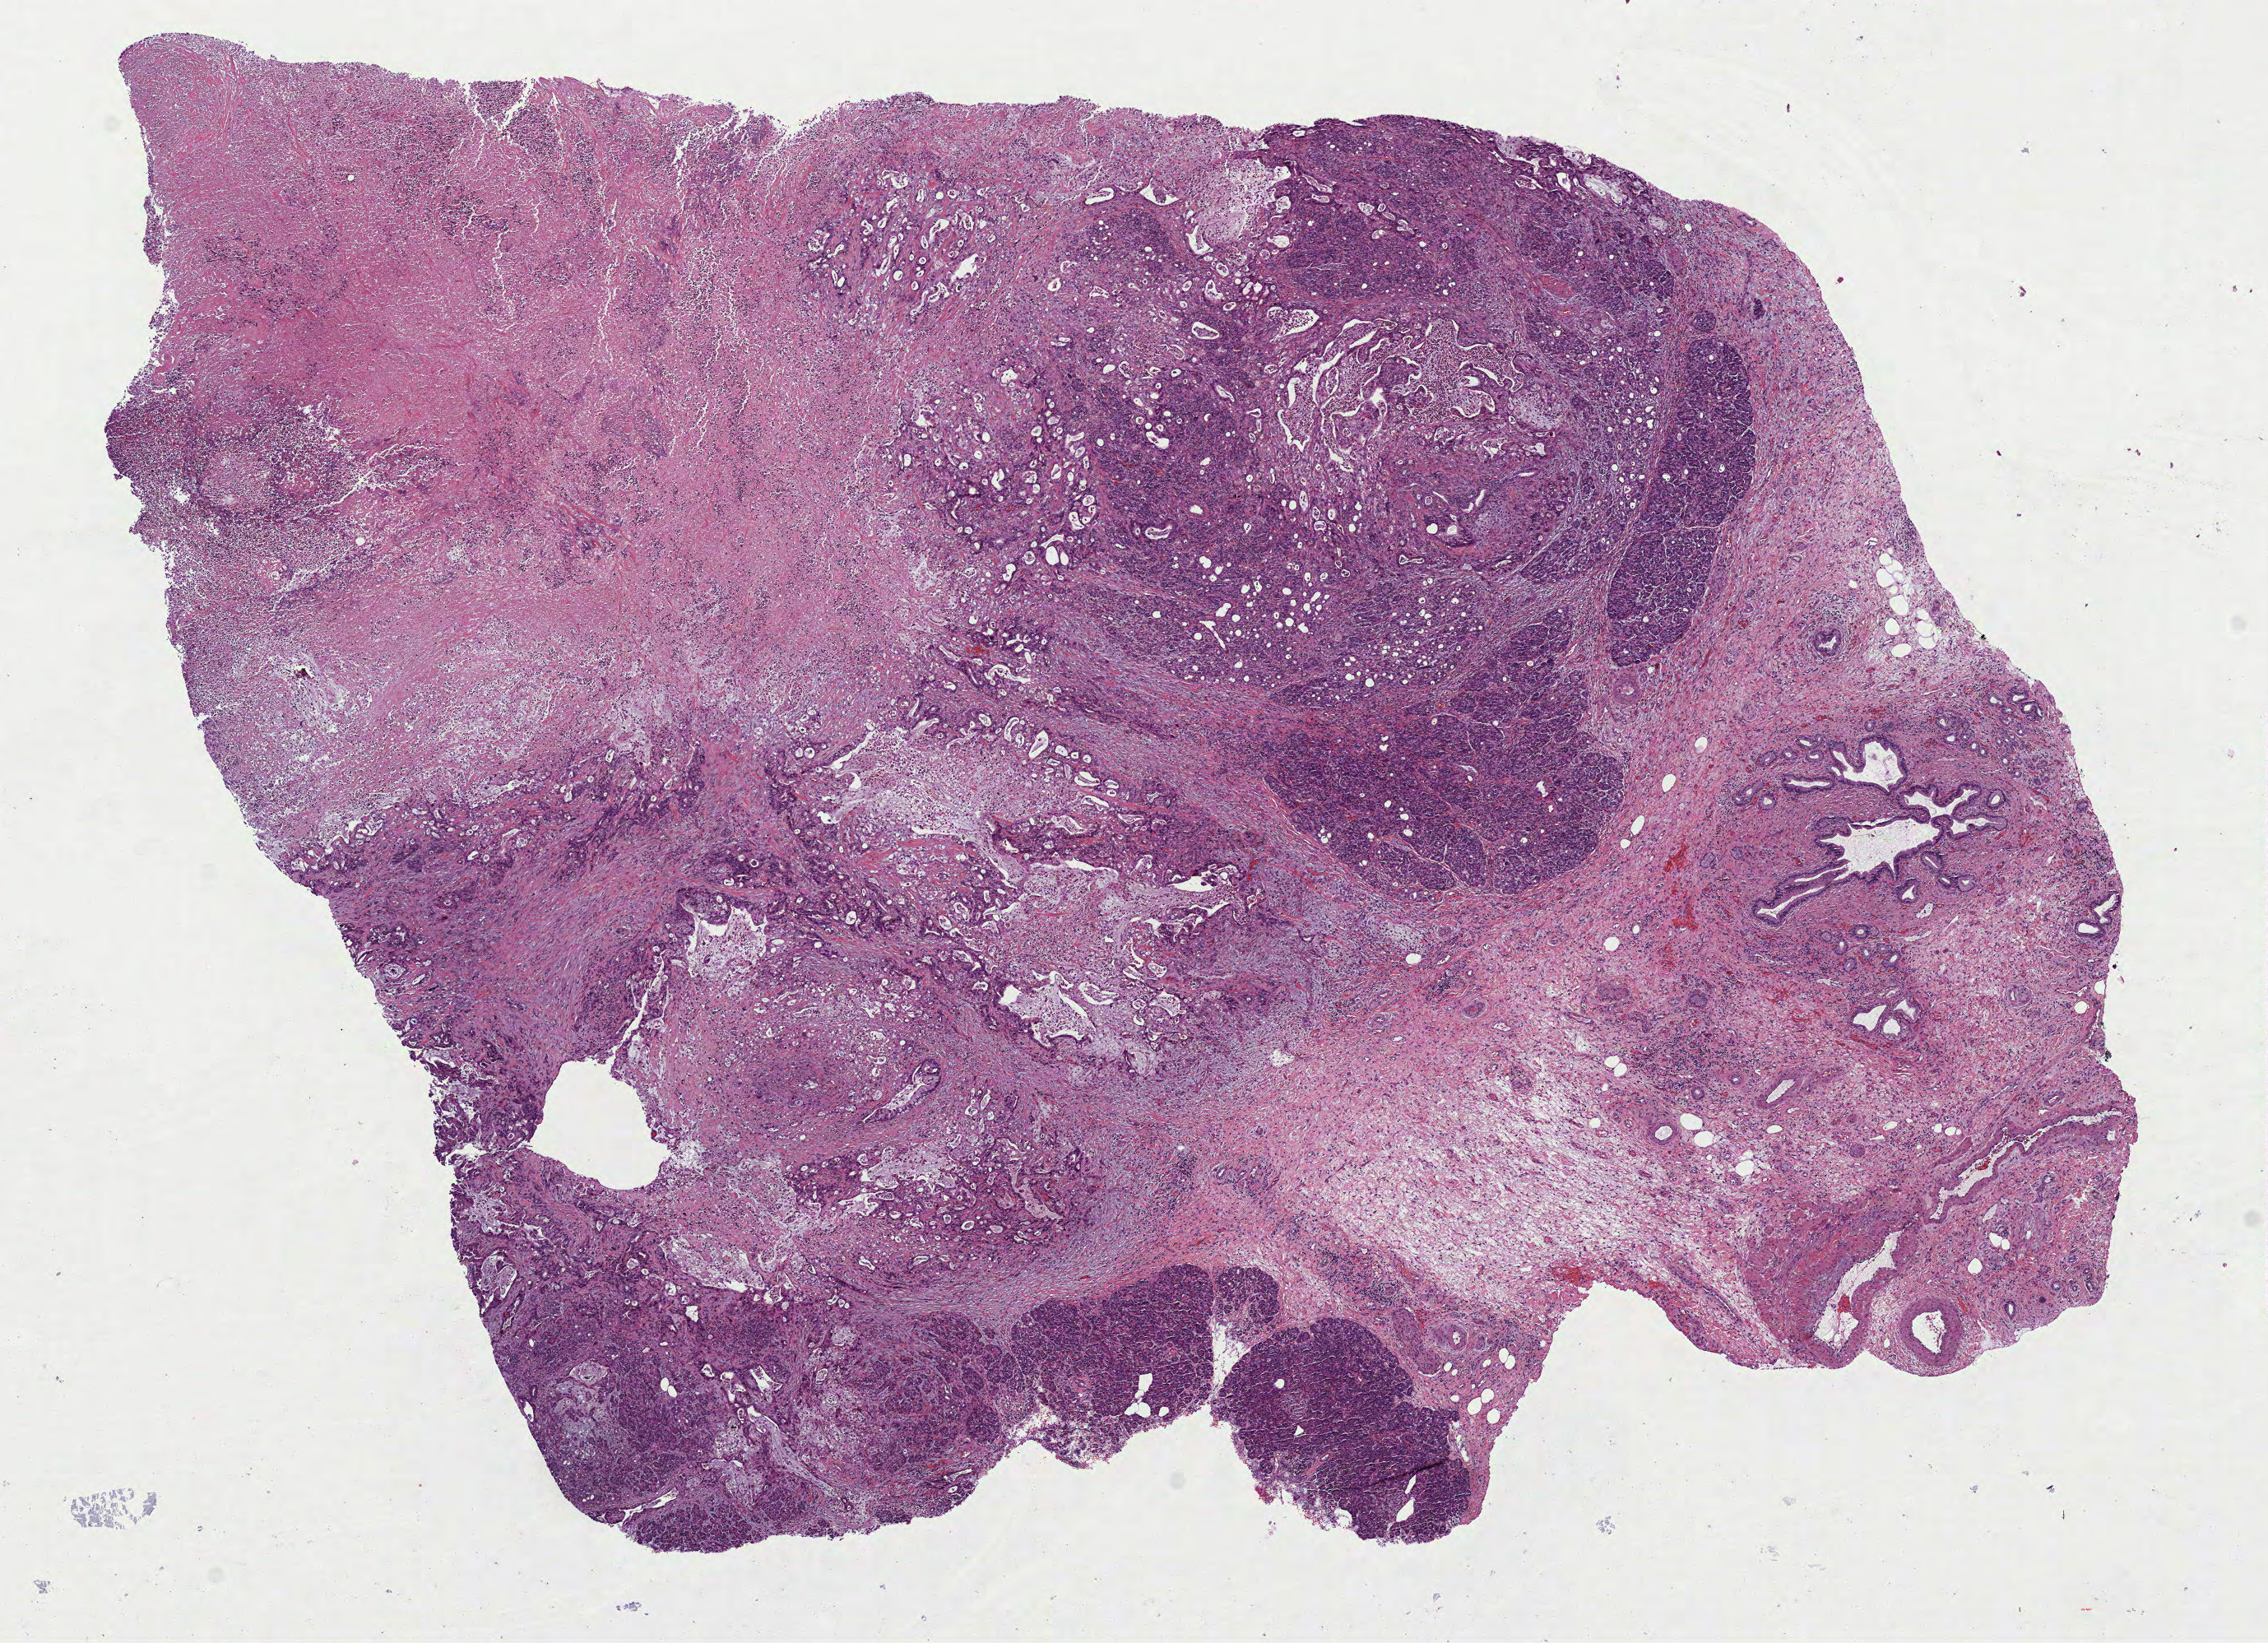
Whole-slide histology image, H&E — shown as a low-resolution overview of the whole scanned area (about 11.1 x 8.1 mm, from a 40x scan), formalin-fixed paraffin-embedded (FFPE) diagnostic section, pancreas, primary tumour sample. Patient: female, age at initial diagnosis 77 years. Histologic grade: G2 (moderately differentiated).
Lymph nodes positive (case pathology): 4 of 26 examined. Histologic diagnosis: Infiltrating duct carcinoma, NOS (head of pancreas). AJCC pathologic stage: IIB. TNM: T2 N1 MX.